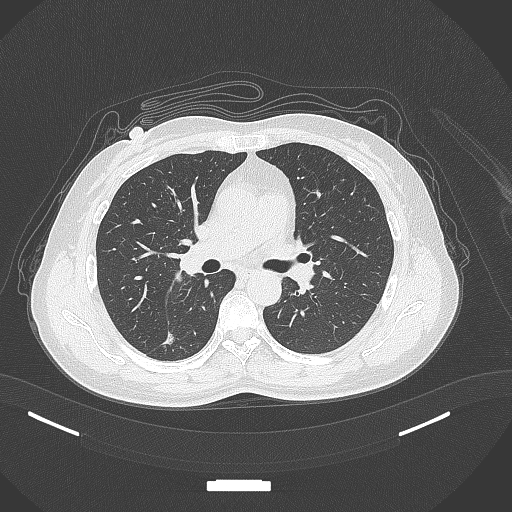
Chest CT, one axial slice; slice 179 of 352 in the series (ordered by position); reconstruction kernel B70f; lung window (W 1500 / L -600 HU); 1 mm slice thickness; 512 × 512 image matrix, field of view 400 × 400 mm. Female patient, age 55 years. Case-level facts recorded for this patient, not image findings: clinical TNM (as recorded): T1c N1 M0.
Outlined on this slice (bounding box drawn by a radiologist):
- lung tumour (recorded histology: adenocarcinoma): bounding box <157,328,180,352> (left, top, right, bottom; pixels)